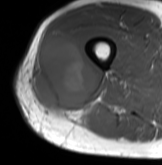
MRI of an extremity soft-tissue mass, one axial slice; slice 36 of 61 in the series (ordered by position); MR volume resampled by the dataset authors to the PET/CT grid (not the native acquisition matrix); 3.27 mm slice thickness; 162 × 165 image matrix, field of view 158 × 161 mm. Male patient. From the clinical record (not read from this slice): histological type: poorly differentiated synovial sarcoma; grade: high; site of the primary tumour: right buttock.
Outlined on this slice (expert contour drawn on MRI and transferred to this co-registered scan by the dataset authors):
- gross tumour volume including surrounding oedema: bounding box <34,36,97,115> (left, top, right, bottom; pixels)
- gross tumour volume (mass): <34,36,97,115>